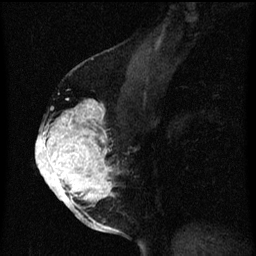
Breast MRI (dynamic contrast-enhanced), one sagittal slice; position 34 of 60 along the scan axis; dynamic contrast-enhanced series, image 2 of 3 at this slice position (ordered by acquisition); 1.5 T; TE 4.2 ms, TR 8 ms; 2 mm slice thickness; 256 × 256 image matrix. Patient: female, 56 years.
Outlined on this slice (semi-automatic segmentation, software-assisted and operator-edited):
- analysis volume of interest (the breast-tissue region the enhancement analysis was run in; not a lesion): box from (x=40, y=100) to (x=123, y=207) px
- tumour enhancement mask (voxels above the 70 % enhancement threshold inside the analysis volume of interest): (x=40, y=100)–(x=113, y=207)